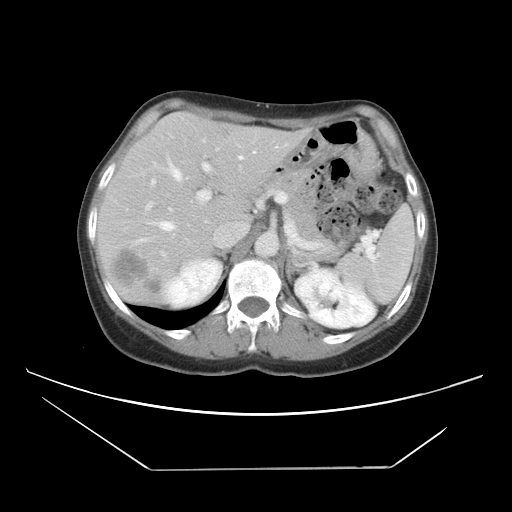
Contrast-enhanced abdominal CT, one axial slice; position 29 of 42 along the scan axis; 120 kVp; intravenous contrast given; soft-tissue window (W 400 / L 40 HU); 512 × 512 image matrix. Female patient, age 52 years. Case-level facts recorded for this patient, not image findings: diagnosis: colorectal cancer liver metastases, imaged before liver resection; multiple liver metastases: yes; largest metastasis: 5.5 cm; disease in both lobes: yes.
Structures marked on this image (expert manual segmentation):
- hepatic veins: bounding box <126,146,278,244> (left, top, right, bottom; pixels)
- liver: <96,114,300,304>
- planned liver remnant (the part of the liver to remain after resection): <114,114,236,225>
- portal vein (with intrahepatic branches): <145,147,292,224>
- liver metastasis: <114,250,161,292>